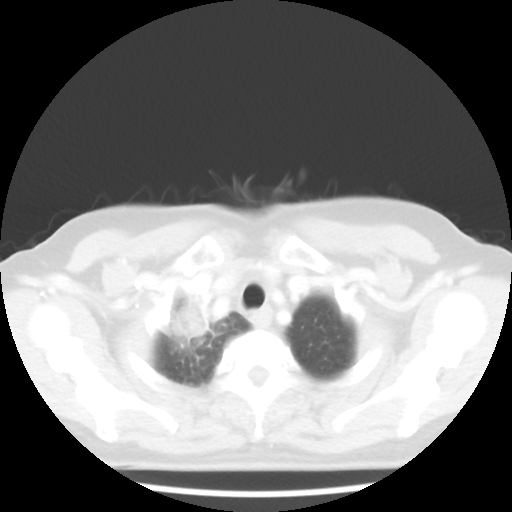
Chest CT, one axial slice. Slice 40 of 44 in the series (ordered by position). 100 kVp. Lung window (W 1500 / L -600 HU). 5 mm slice thickness. 512 × 512 image matrix, field of view 316 × 316 mm. Female patient, age 62 years. Case-level facts recorded for this patient, not image findings: clinical TNM (as recorded): T3 N0 M0.
Annotated regions visible in this slice (bounding box drawn by a radiologist):
- lung tumour (recorded histology: small cell carcinoma): bounding box [x1, y1, x2, y2] px = [170, 288, 212, 342]